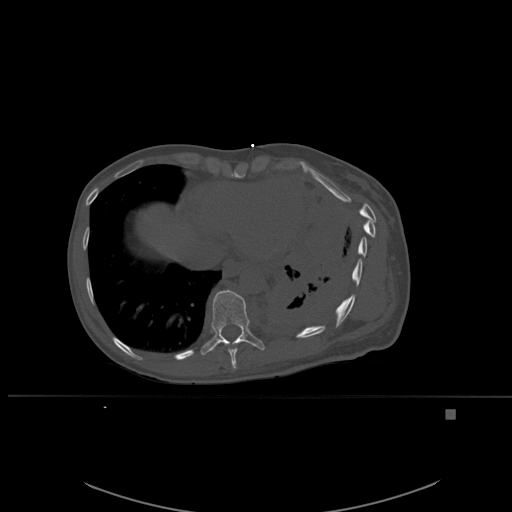
CT including the spine, one axial slice; position 322 of 537 along the scan axis; bone window (W 1800 / L 400 HU); 1.5 mm slice thickness; 512 × 512 image matrix, field of view 440 × 440 mm. Female patient, age 45 years. From the clinical record (not read from this slice): primary cancer: lung.
Structures marked on this image (semi-automatic segmentation, software-assisted and operator-edited):
- T10 vertebra: bounding box [x1, y1, x2, y2] px = [200, 290, 265, 355]
- T9 vertebra: [228, 341, 238, 369]